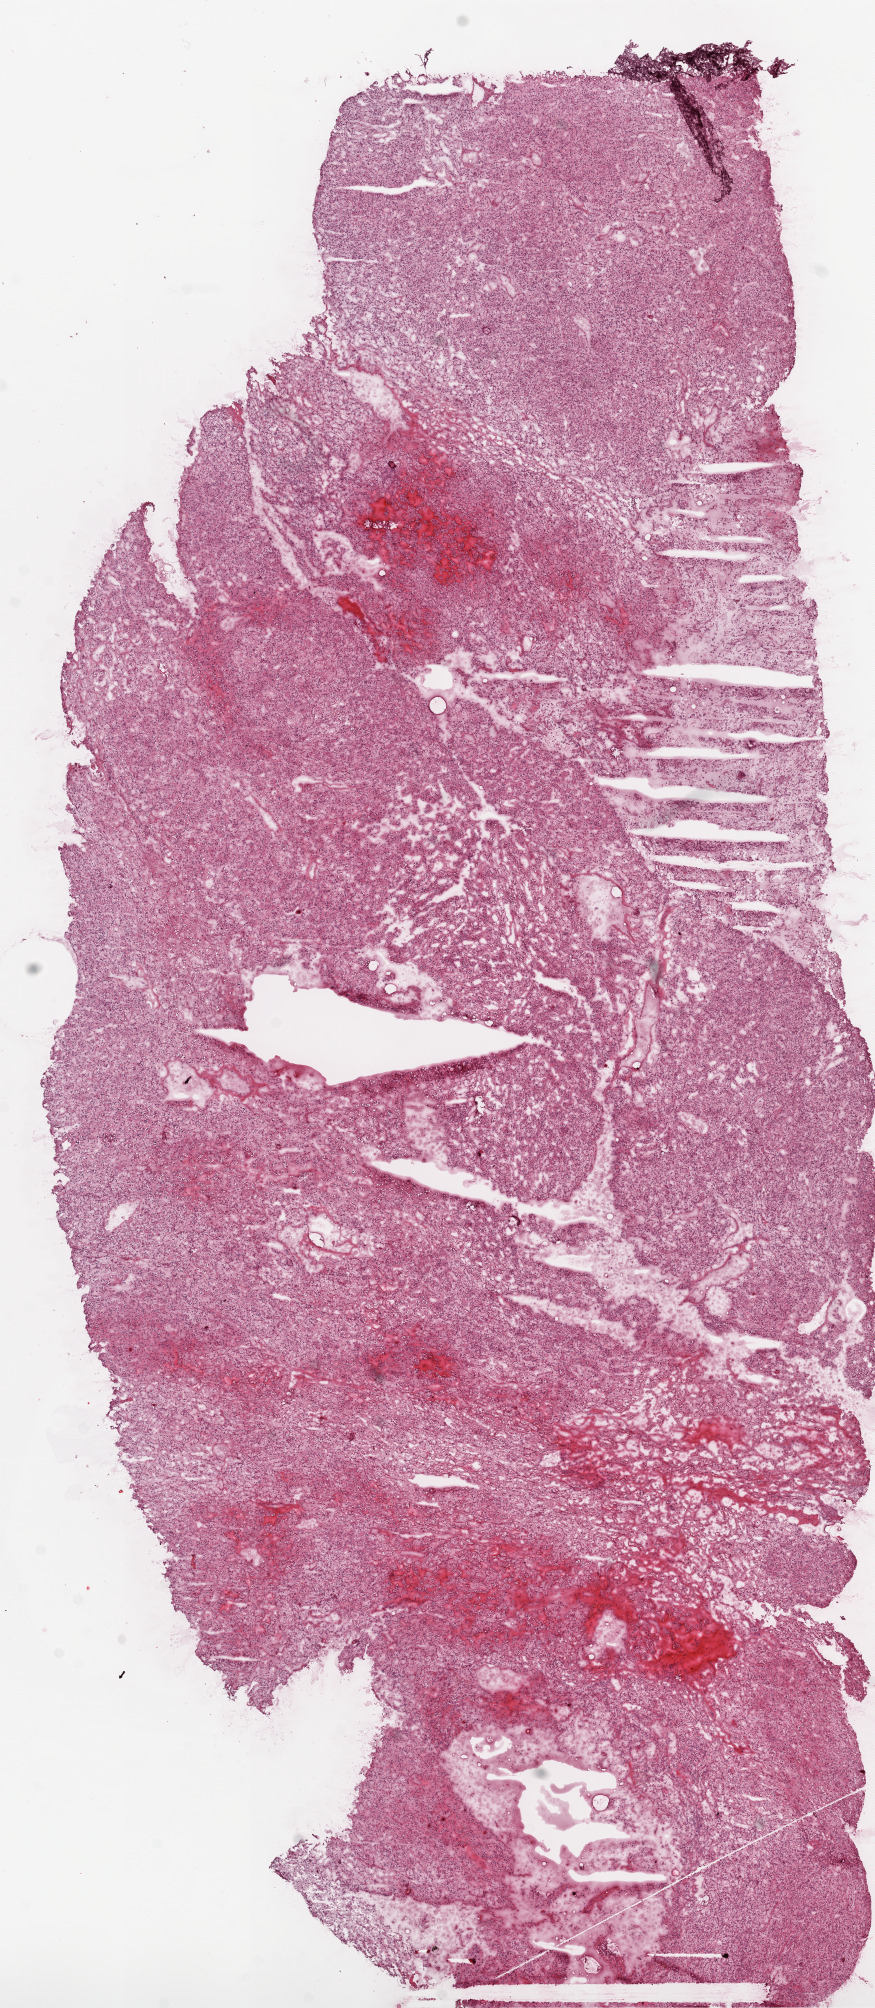
H&E-stained whole-slide image — a low-resolution overview of the entire scanned area, about 7.0 x 16.1 mm (acquisition: 20x scan); frozen section from the top of the tissue portion; sample: primary tumour, kidney. Female patient; age at initial diagnosis 78 years. Histologic grade: G2 (moderately differentiated). Pathologist review of this section (percent, as recorded): tumour cells 90%, tumour nuclei 90%, normal cells 0%, stromal cells 10%, necrosis 0%.
- AJCC pathologic stage: I
- TNM: T1a NX M0
- diagnosis: Clear cell adenocarcinoma, NOS
- laterality: left